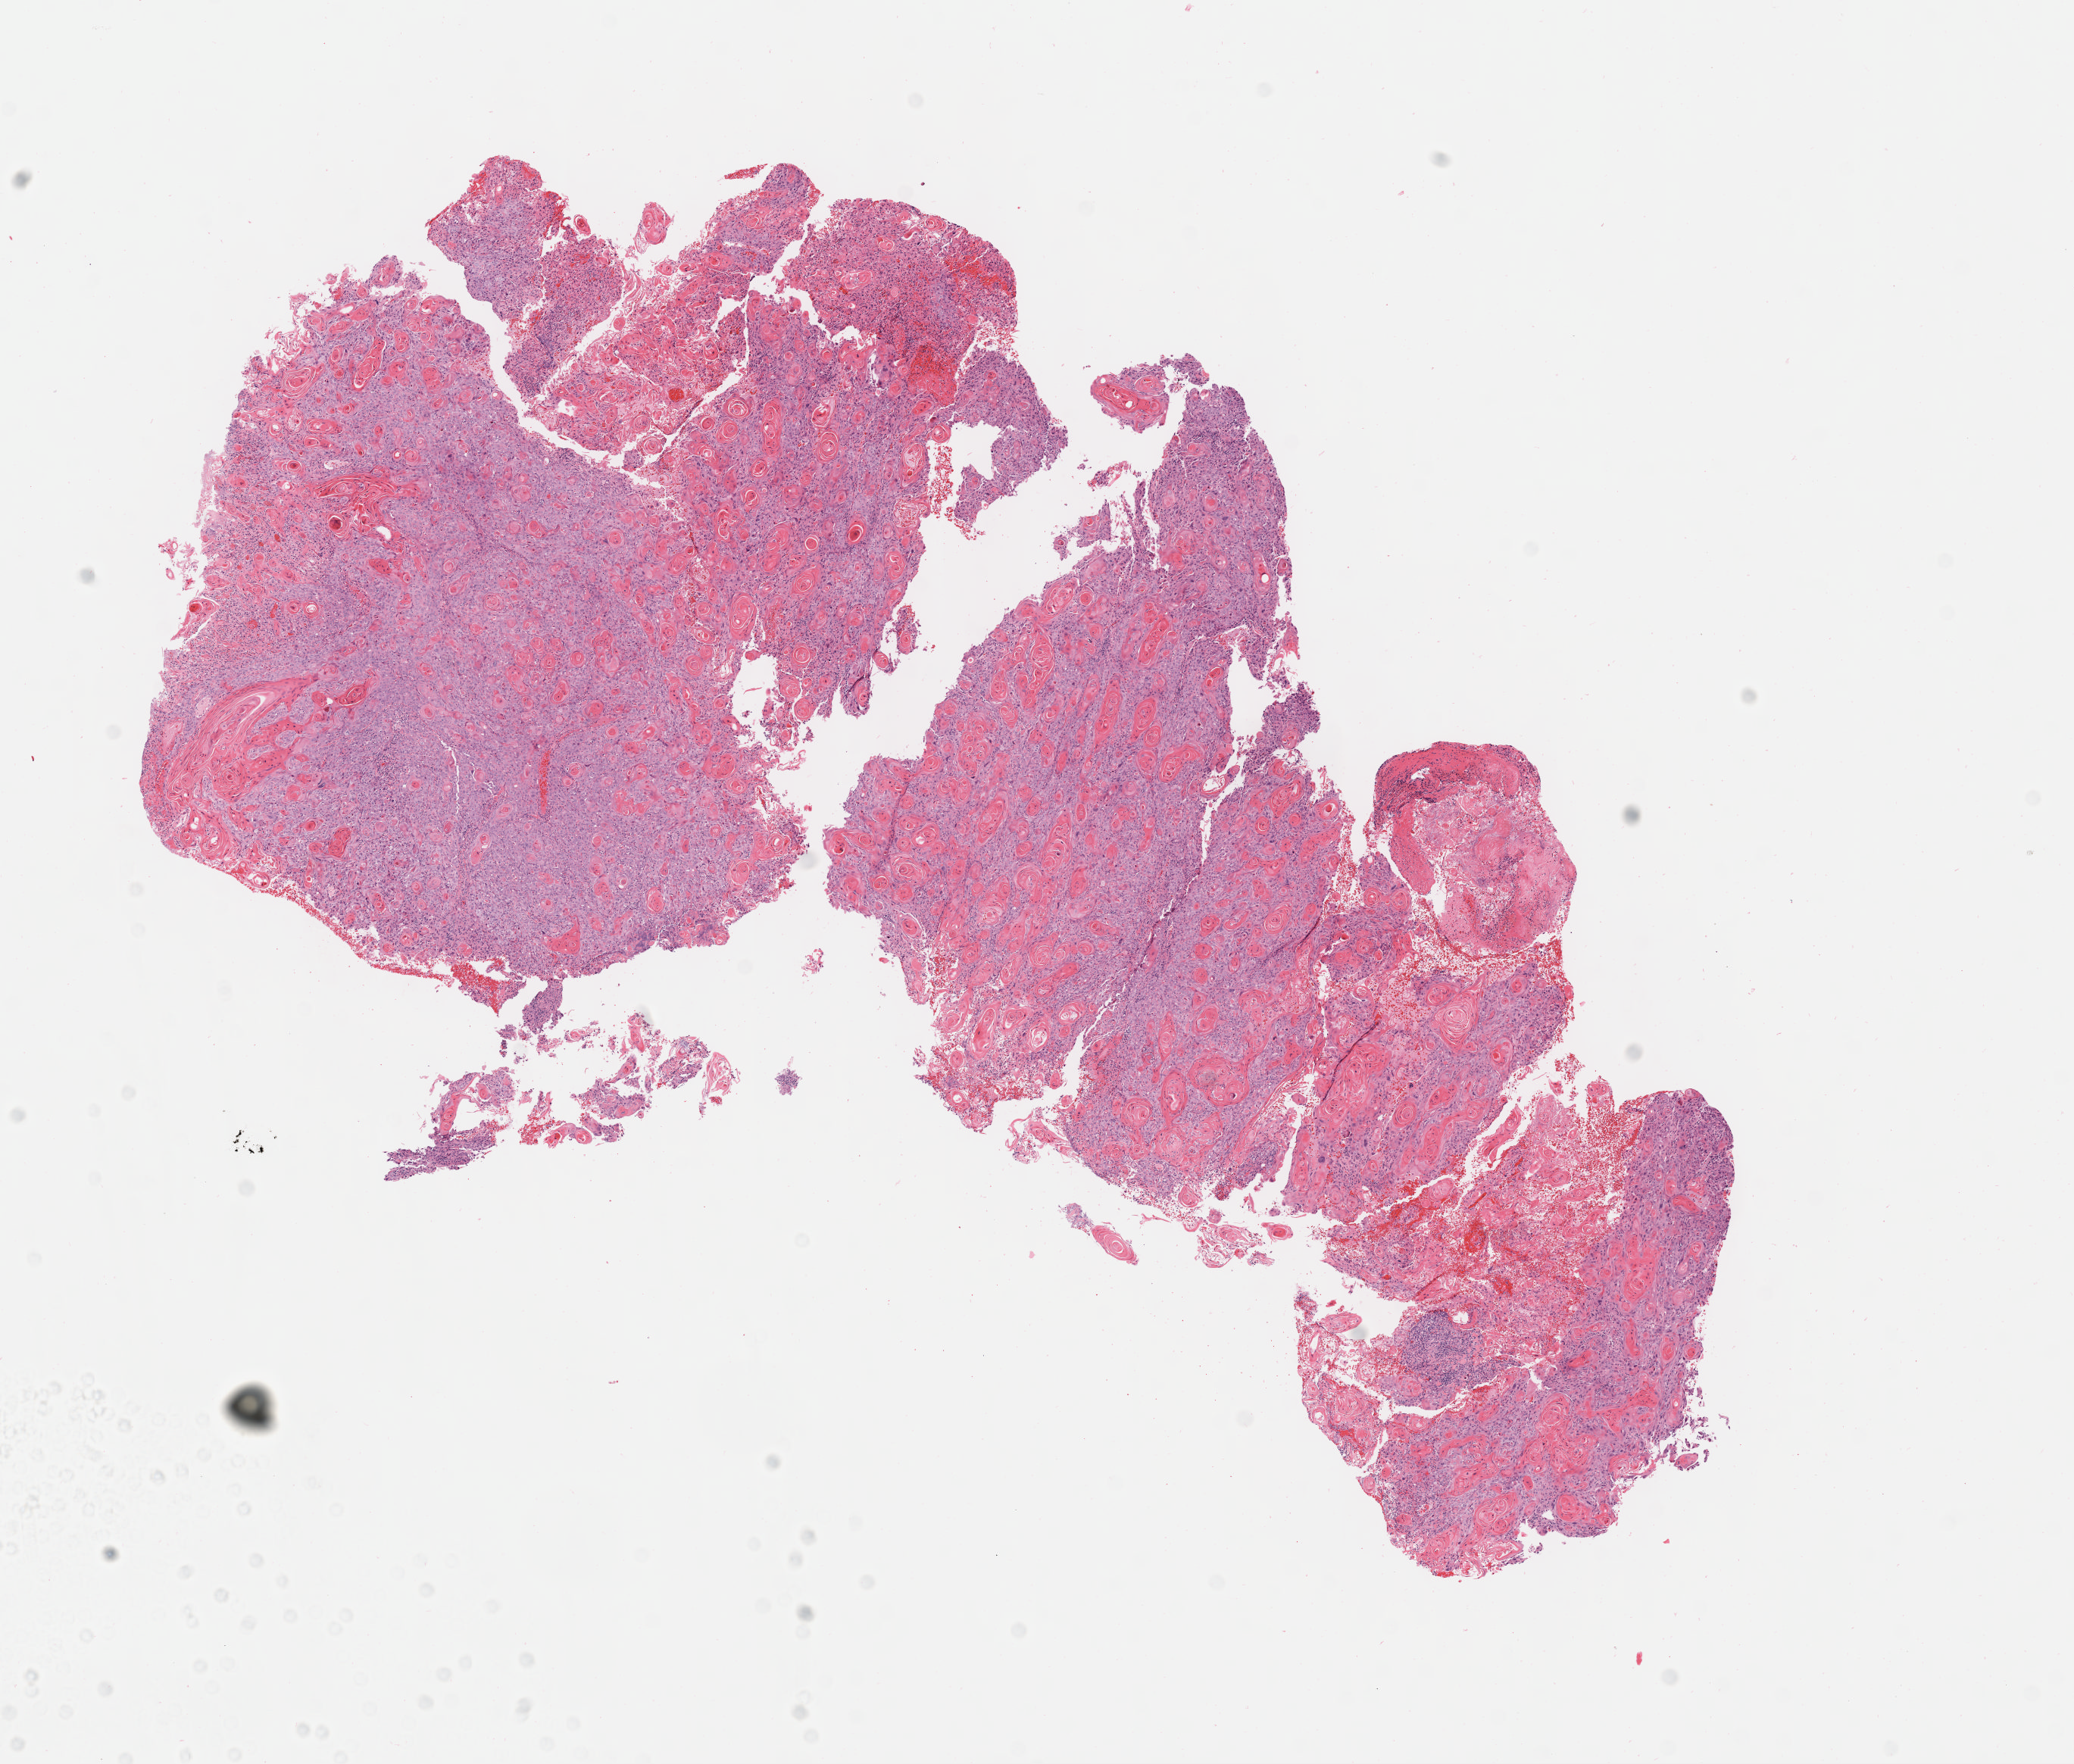
Whole-slide image, H&E stain — shown as a low-resolution overview of the whole scanned area (about 11.1 x 9.4 mm); specimen: tumor tissue; site: cervix. Patient female; 26 years old.
Diagnosis: Squamous cell carcinoma, keratinizing, NOS.